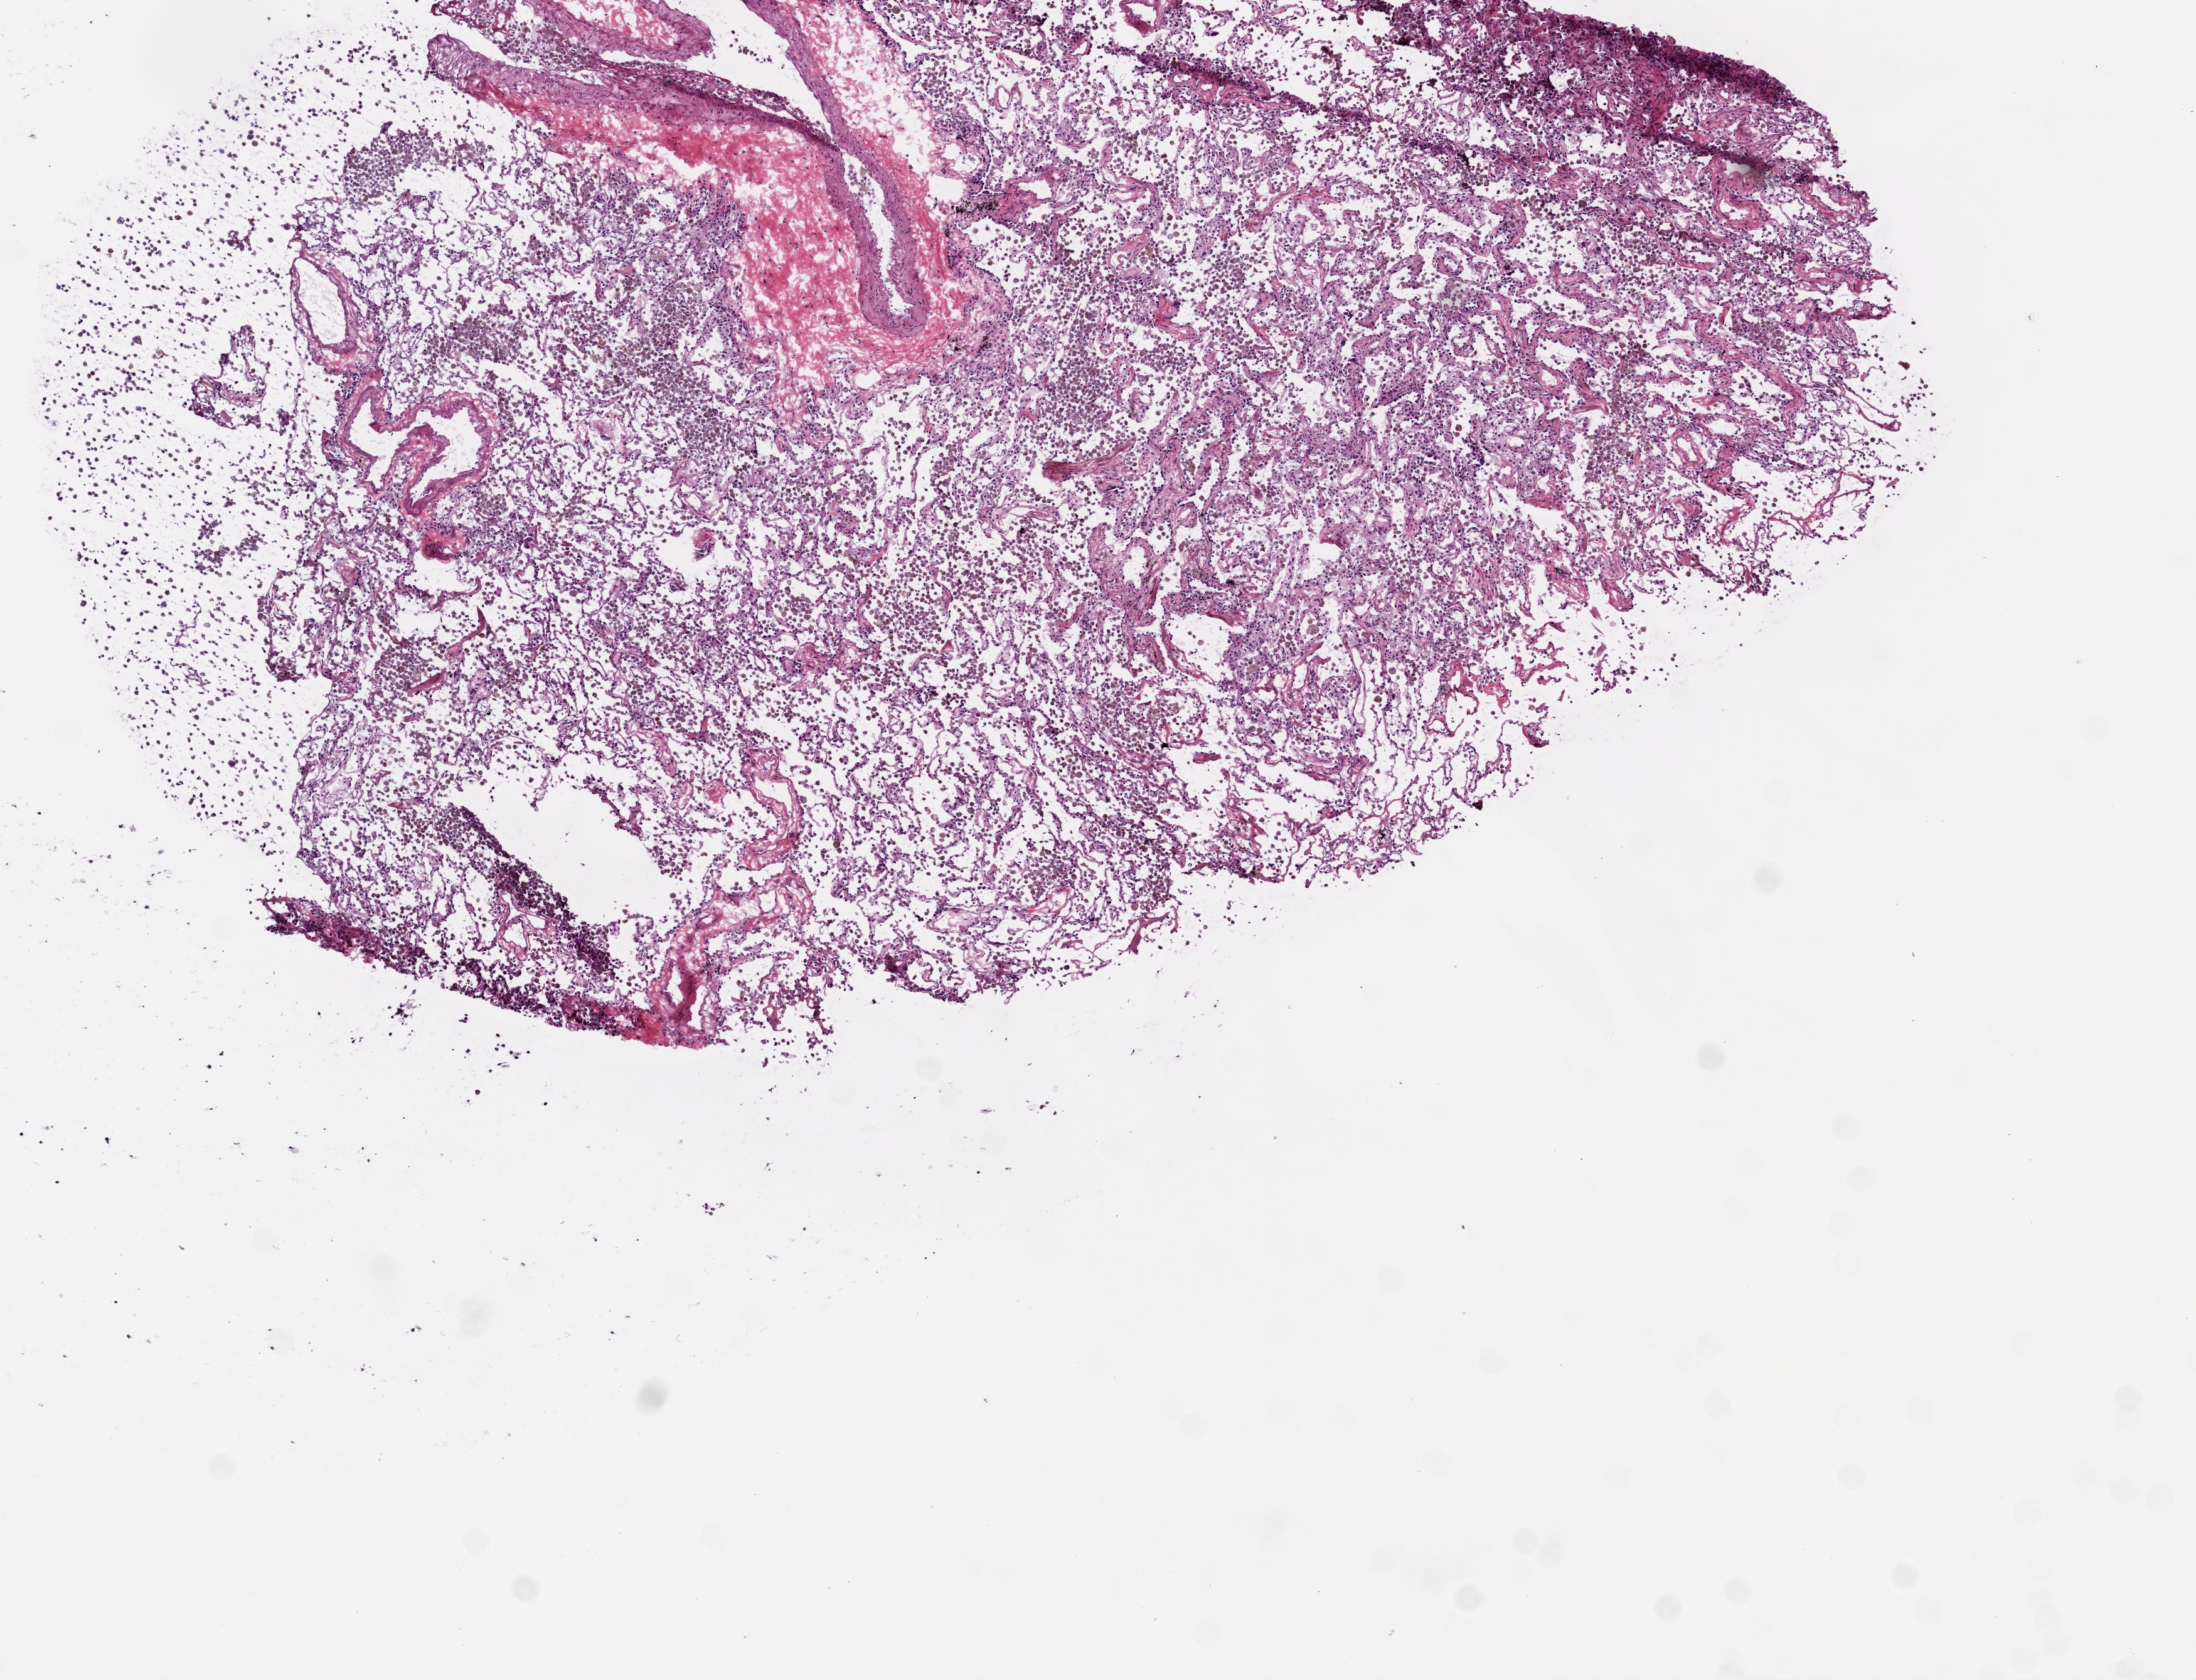
Whole-slide histology image, H&E, whole scanned area (about 7.0 x 5.4 mm, acquisition: 20x scan) shown as a low-resolution overview; frozen section from the top of the tissue portion; solid tissue normal (non-tumour tissue) sample from the lung. Female patient; age at initial diagnosis 57 years.
This section: solid tissue normal sample (biorepository sample class). Patient diagnosis: Adenocarcinoma, NOS.